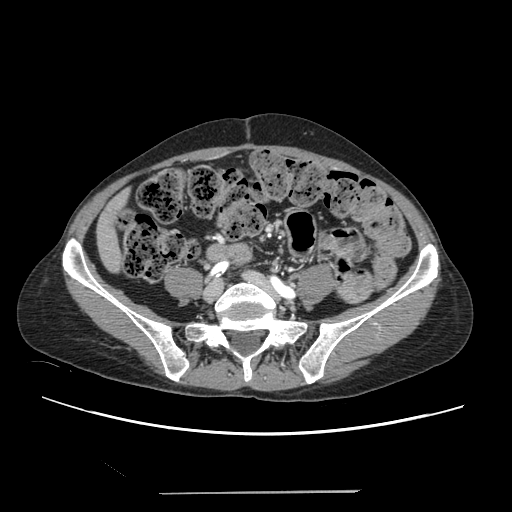
Contrast-enhanced abdominal CT, one axial slice. Position 15 of 240 along the scan axis. Intravenous contrast given. Soft-tissue window (W 400 / L 40 HU). 512 × 512 image matrix, field of view 371 × 371 mm. Female patient, age 60 years. From the clinical record (not read from this slice): diagnosis: colorectal cancer liver metastases, imaged before liver resection; multiple liver metastases: no; largest metastasis: 1.5 cm; disease in both lobes: no.
Annotated regions visible in this slice (outlined manually by an expert reader):
- liver: bounding box (x1, y1, x2, y2) in pixels: (99, 201, 122, 270)
- planned liver remnant (the part of the liver to remain after resection): (99, 199, 122, 270)